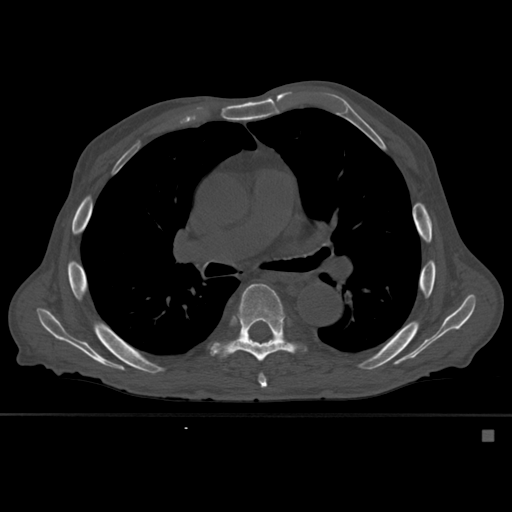
CT including the spine, one axial slice; bone window (W 1800 / L 400 HU); 1.5 mm slice thickness; 512 × 512 image matrix. Patient: male, 78 years. From the clinical record (not read from this slice): primary cancer: prostate.
Annotated regions visible in this slice (semi-automatically segmented with operator editing):
- T6 vertebra: bounding box <258,374,267,388> (left, top, right, bottom; pixels)
- T7 vertebra: <211,283,297,362>